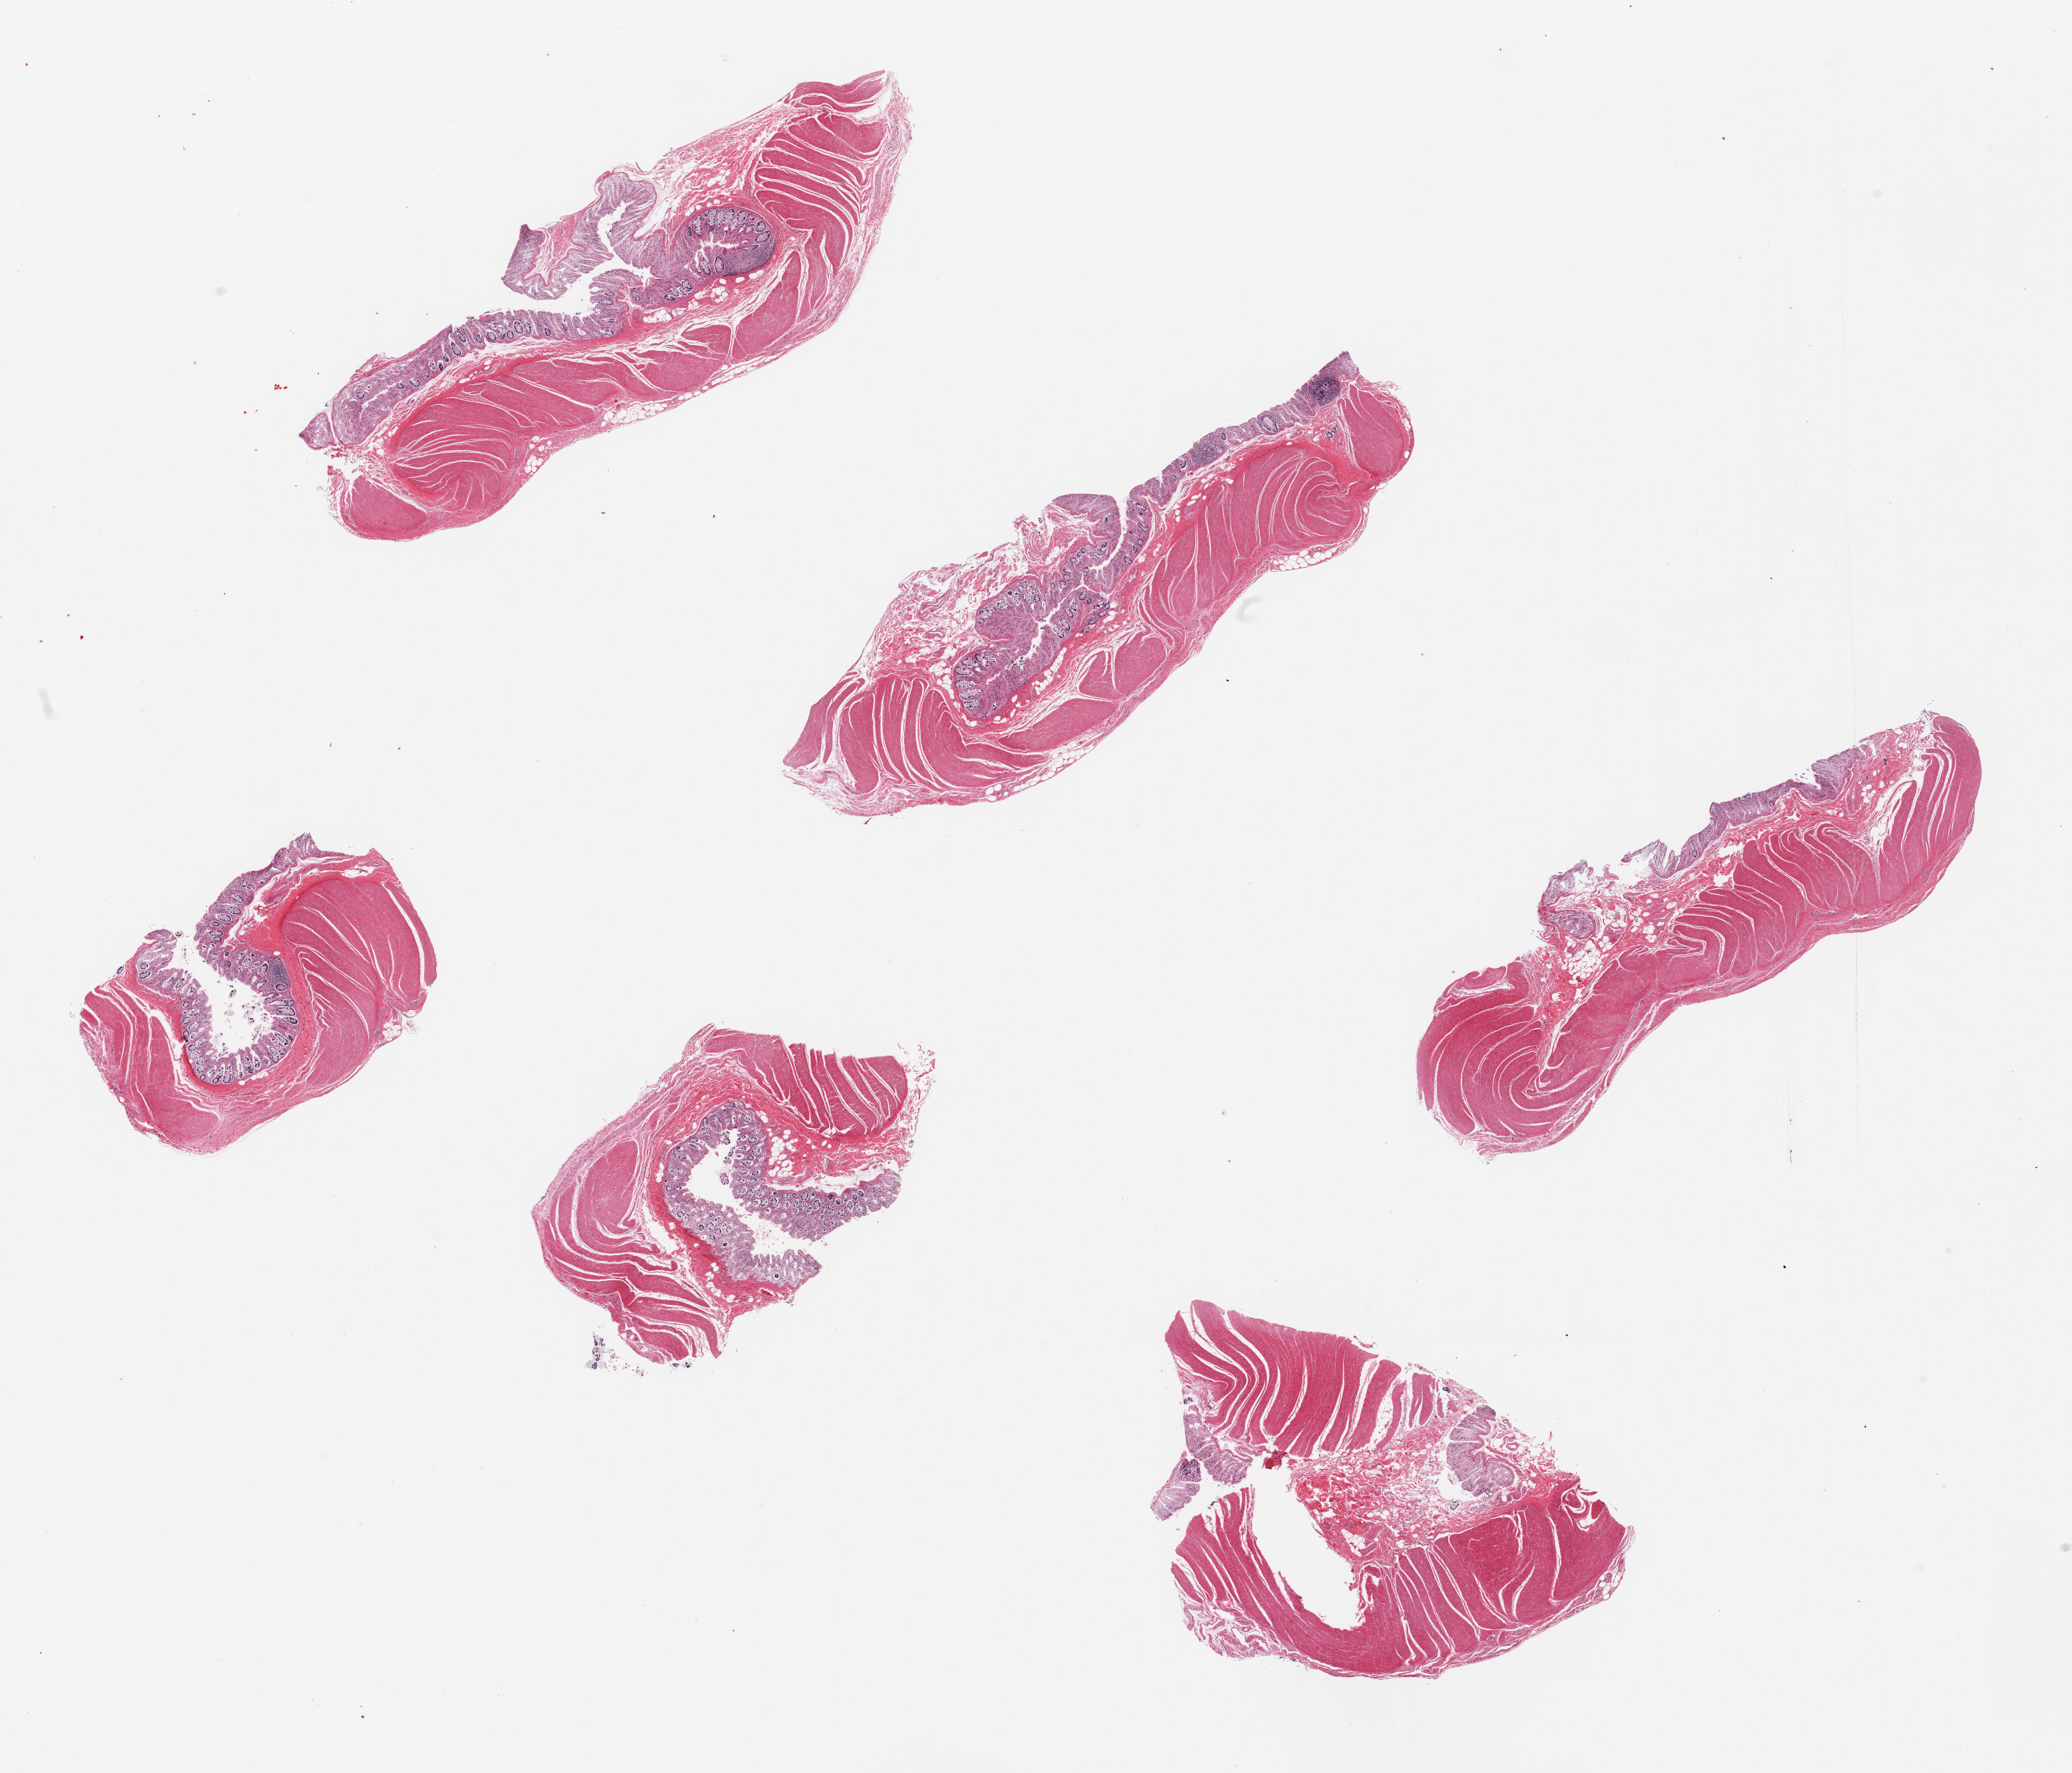
Whole-slide image, hematoxylin and eosin (H&E) stain, brightfield, shown as a low-resolution overview of the whole scanned area (about 24.6 x 21.1 mm, slide scanned at 20x). PAXgene-fixed paraffin-embedded (PFPE) section. Target tissue: sigmoid colon. Tissue donor sample.
Pathologist's review note for this sample: 6 pieces, ~10% 'contaminant' totally autolyzed mucosa.